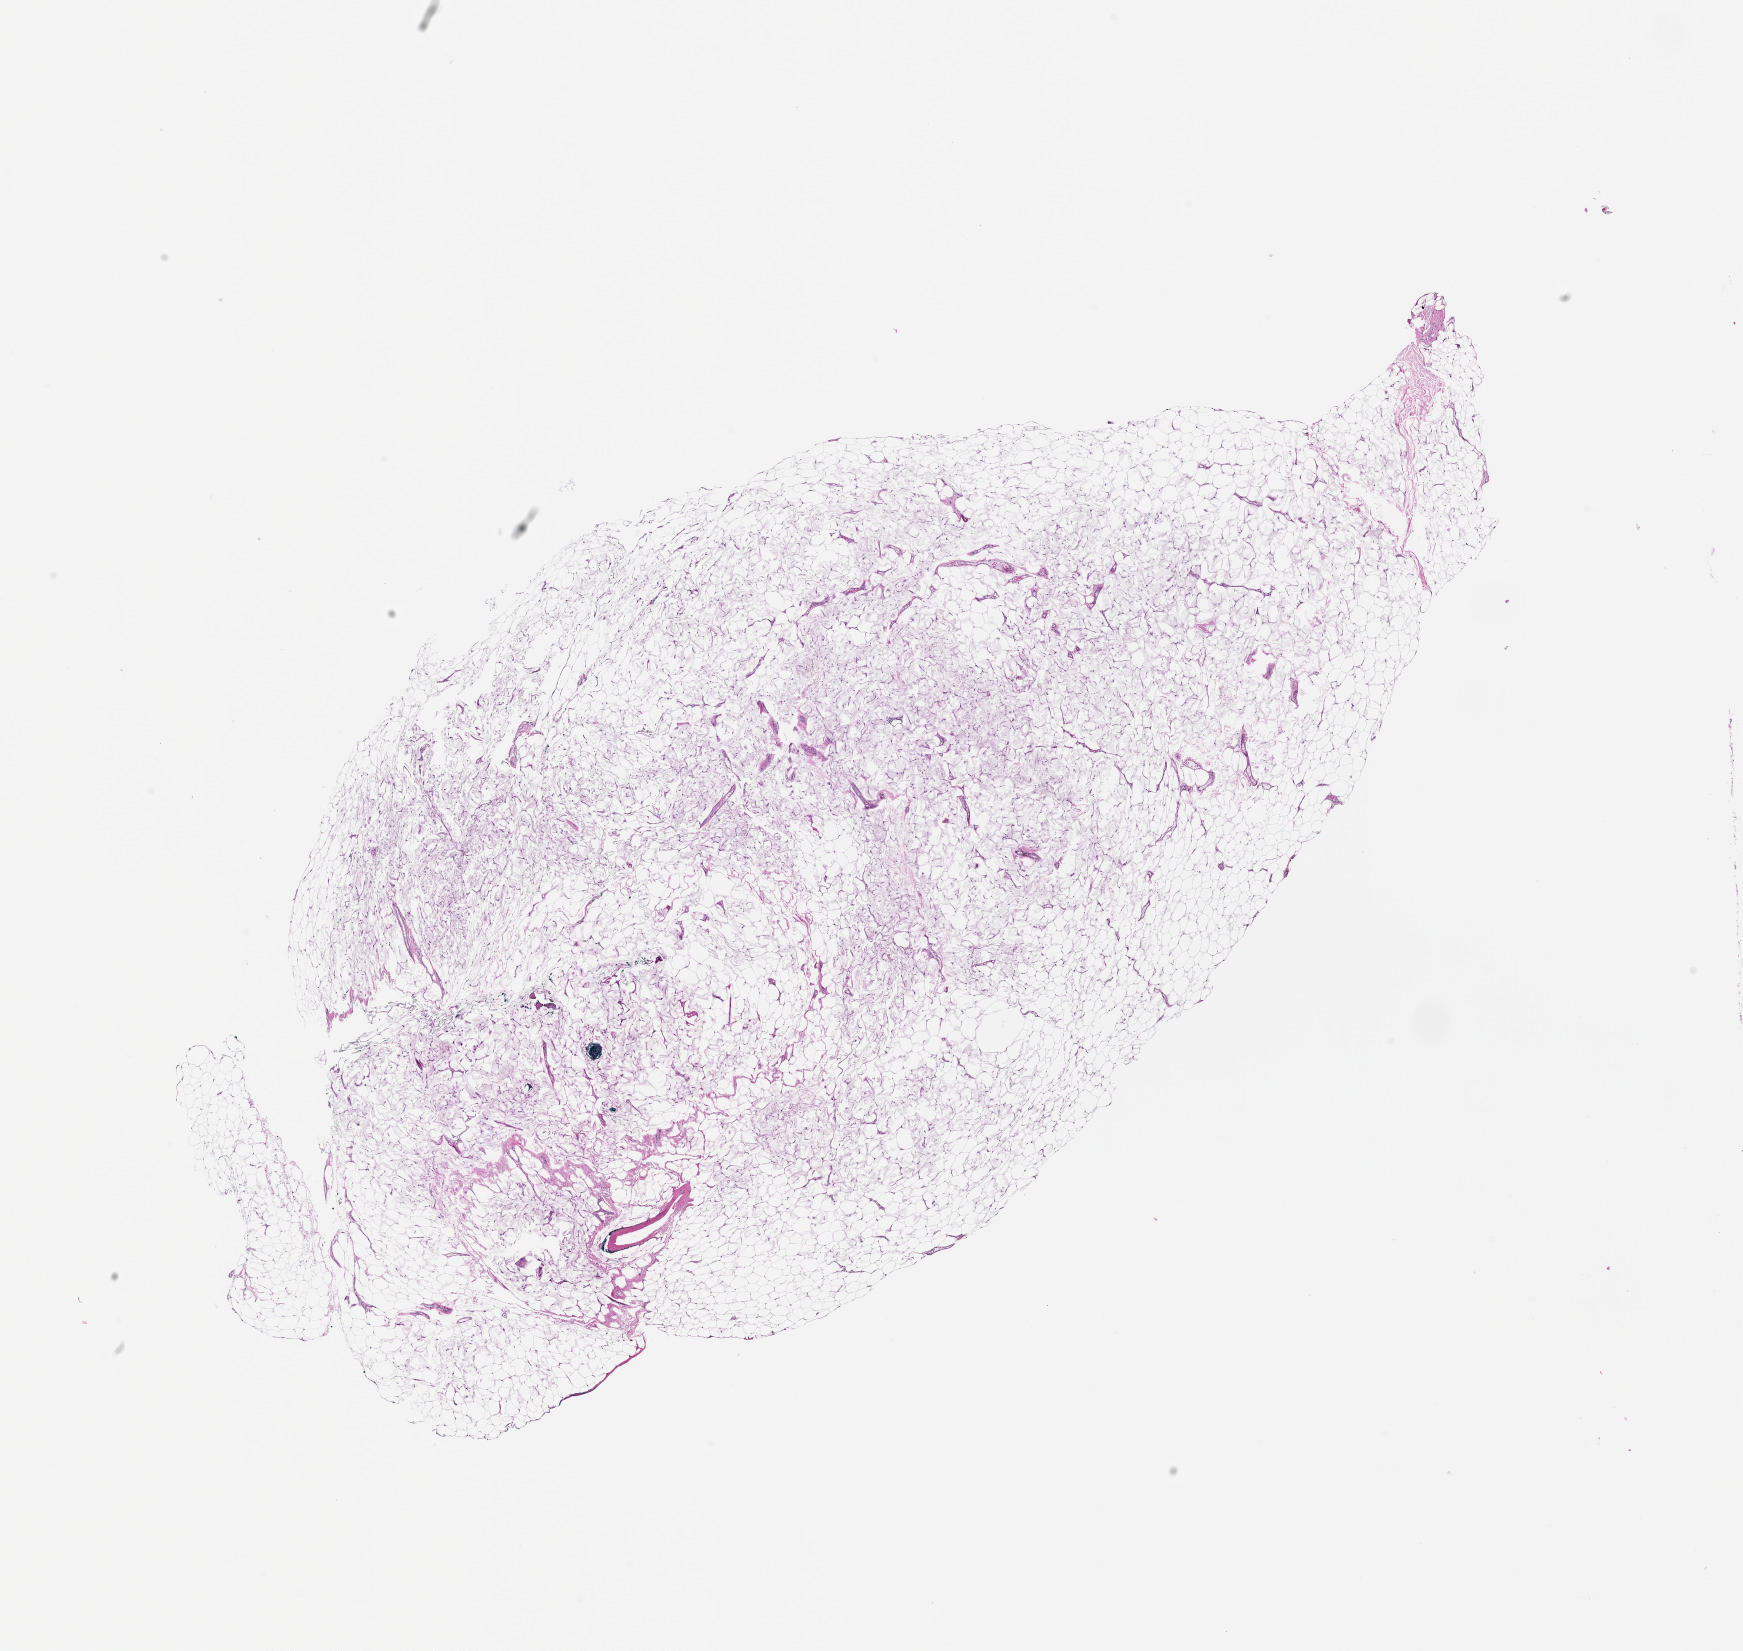
Digitized H&E tissue section (whole slide), shown as a low-resolution overview of the whole scanned area (about 14.0 x 13.3 mm, from a 20x scan).
Patient diagnosis (cohort enrolment): sarcoma (site not recorded at cohort level).